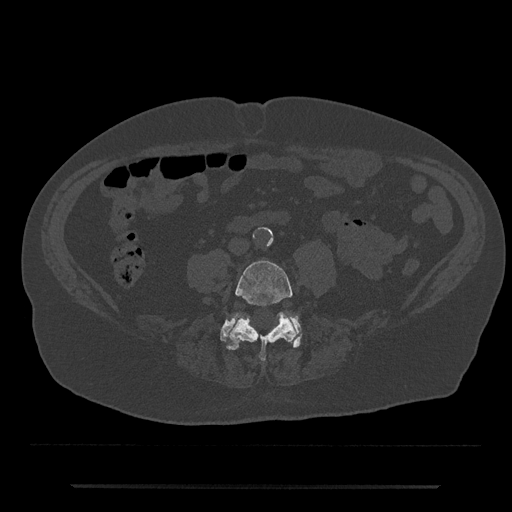
CT including the spine, one axial slice. Position 337 of 797 along the scan axis. 120 kVp. Bone window (W 1800 / L 400 HU). 512 × 512 image matrix. Patient: male, 80 years. Case-level facts recorded for this patient, not image findings: primary cancer: prostate; vertebrae with lytic lesions (as recorded): L1, T11.
Structures marked on this image (semi-automatically segmented with operator editing):
- L4 vertebra: bounding box [x1, y1, x2, y2] px = [227, 260, 297, 361]
- L5 vertebra: [220, 314, 302, 350]